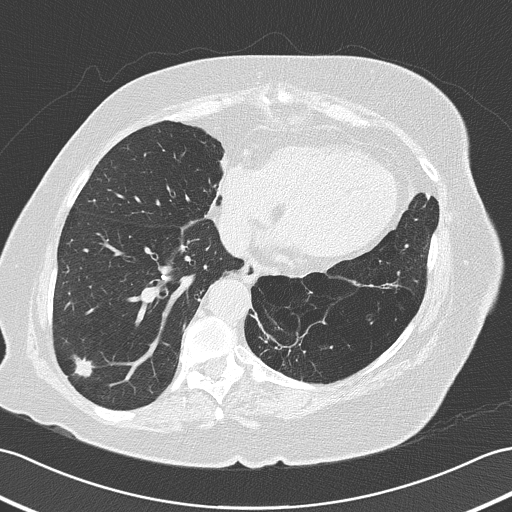
Axial slice from a low-dose chest CT screening exam; baseline screening round; lung window (W 1500 / L -600 HU); lung (sharp) reconstruction kernel (B50f); slice 101 of 161 in the series. Female participant, aged 73 years at enrolment.
Lesion marked by an expert reader, bounding box (x1, y1, x2, y2) in pixels: (54, 337, 101, 385). The screening reader recorded 4 non-calcified nodules or masses ≥4 mm on this exam (right lower lobe, right upper lobe, left upper lobe, left lower lobe); which of them this box marks is not recorded. Participant outcome: lung cancer diagnosed 50 days after this screen — adenocarcinoma, NOS, right lower lobe, poorly differentiated (G3), stage IB (AJCC 6th edition), 17 mm at pathology.